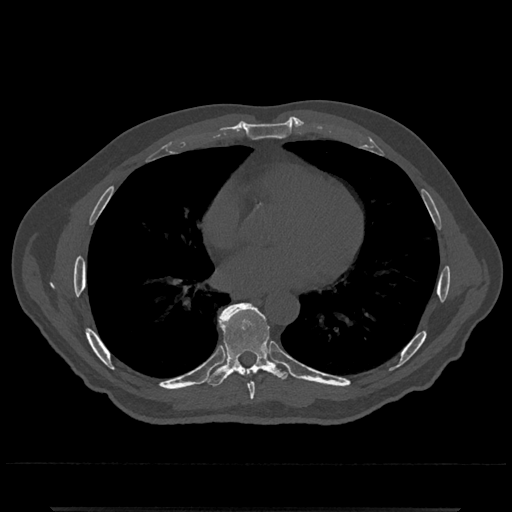
CT including the spine, one axial slice; position 685 of 797 along the scan axis; bone window (W 1800 / L 400 HU); 0.5 mm slice thickness; 512 × 512 image matrix, field of view 393 × 393 mm. Male patient, age 67 years. From the clinical record (not read from this slice): primary cancer: prostate.
Annotated regions visible in this slice (semi-automatically segmented with operator editing):
- T7 vertebra: bounding box <248,383,255,402> (left, top, right, bottom; pixels)
- T8 vertebra: <203,303,291,387>